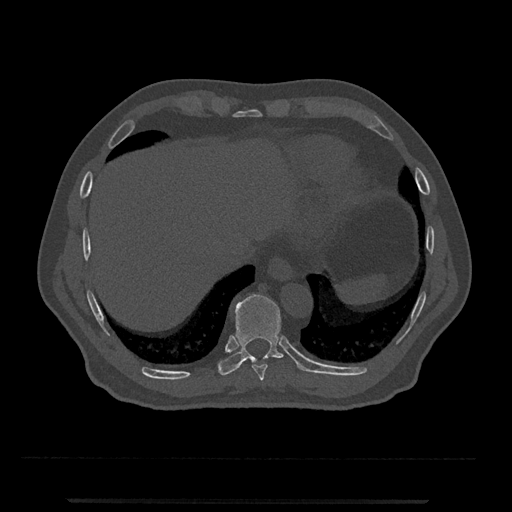
CT including the spine, one axial slice; slice 539 of 797 in the series (ordered by position); reconstruction kernel Br40s/3; 120 kVp; bone window (W 1800 / L 400 HU); 0.5 mm slice thickness; 512 × 512 image matrix. Male patient, age 63 years. Case-level facts recorded for this patient, not image findings: primary cancer: prostate.
Outlined on this slice (semi-automatically segmented with operator editing):
- T10 vertebra: box from (x=218, y=294) to (x=284, y=375) px
- T9 vertebra: (x=252, y=364)–(x=268, y=381)